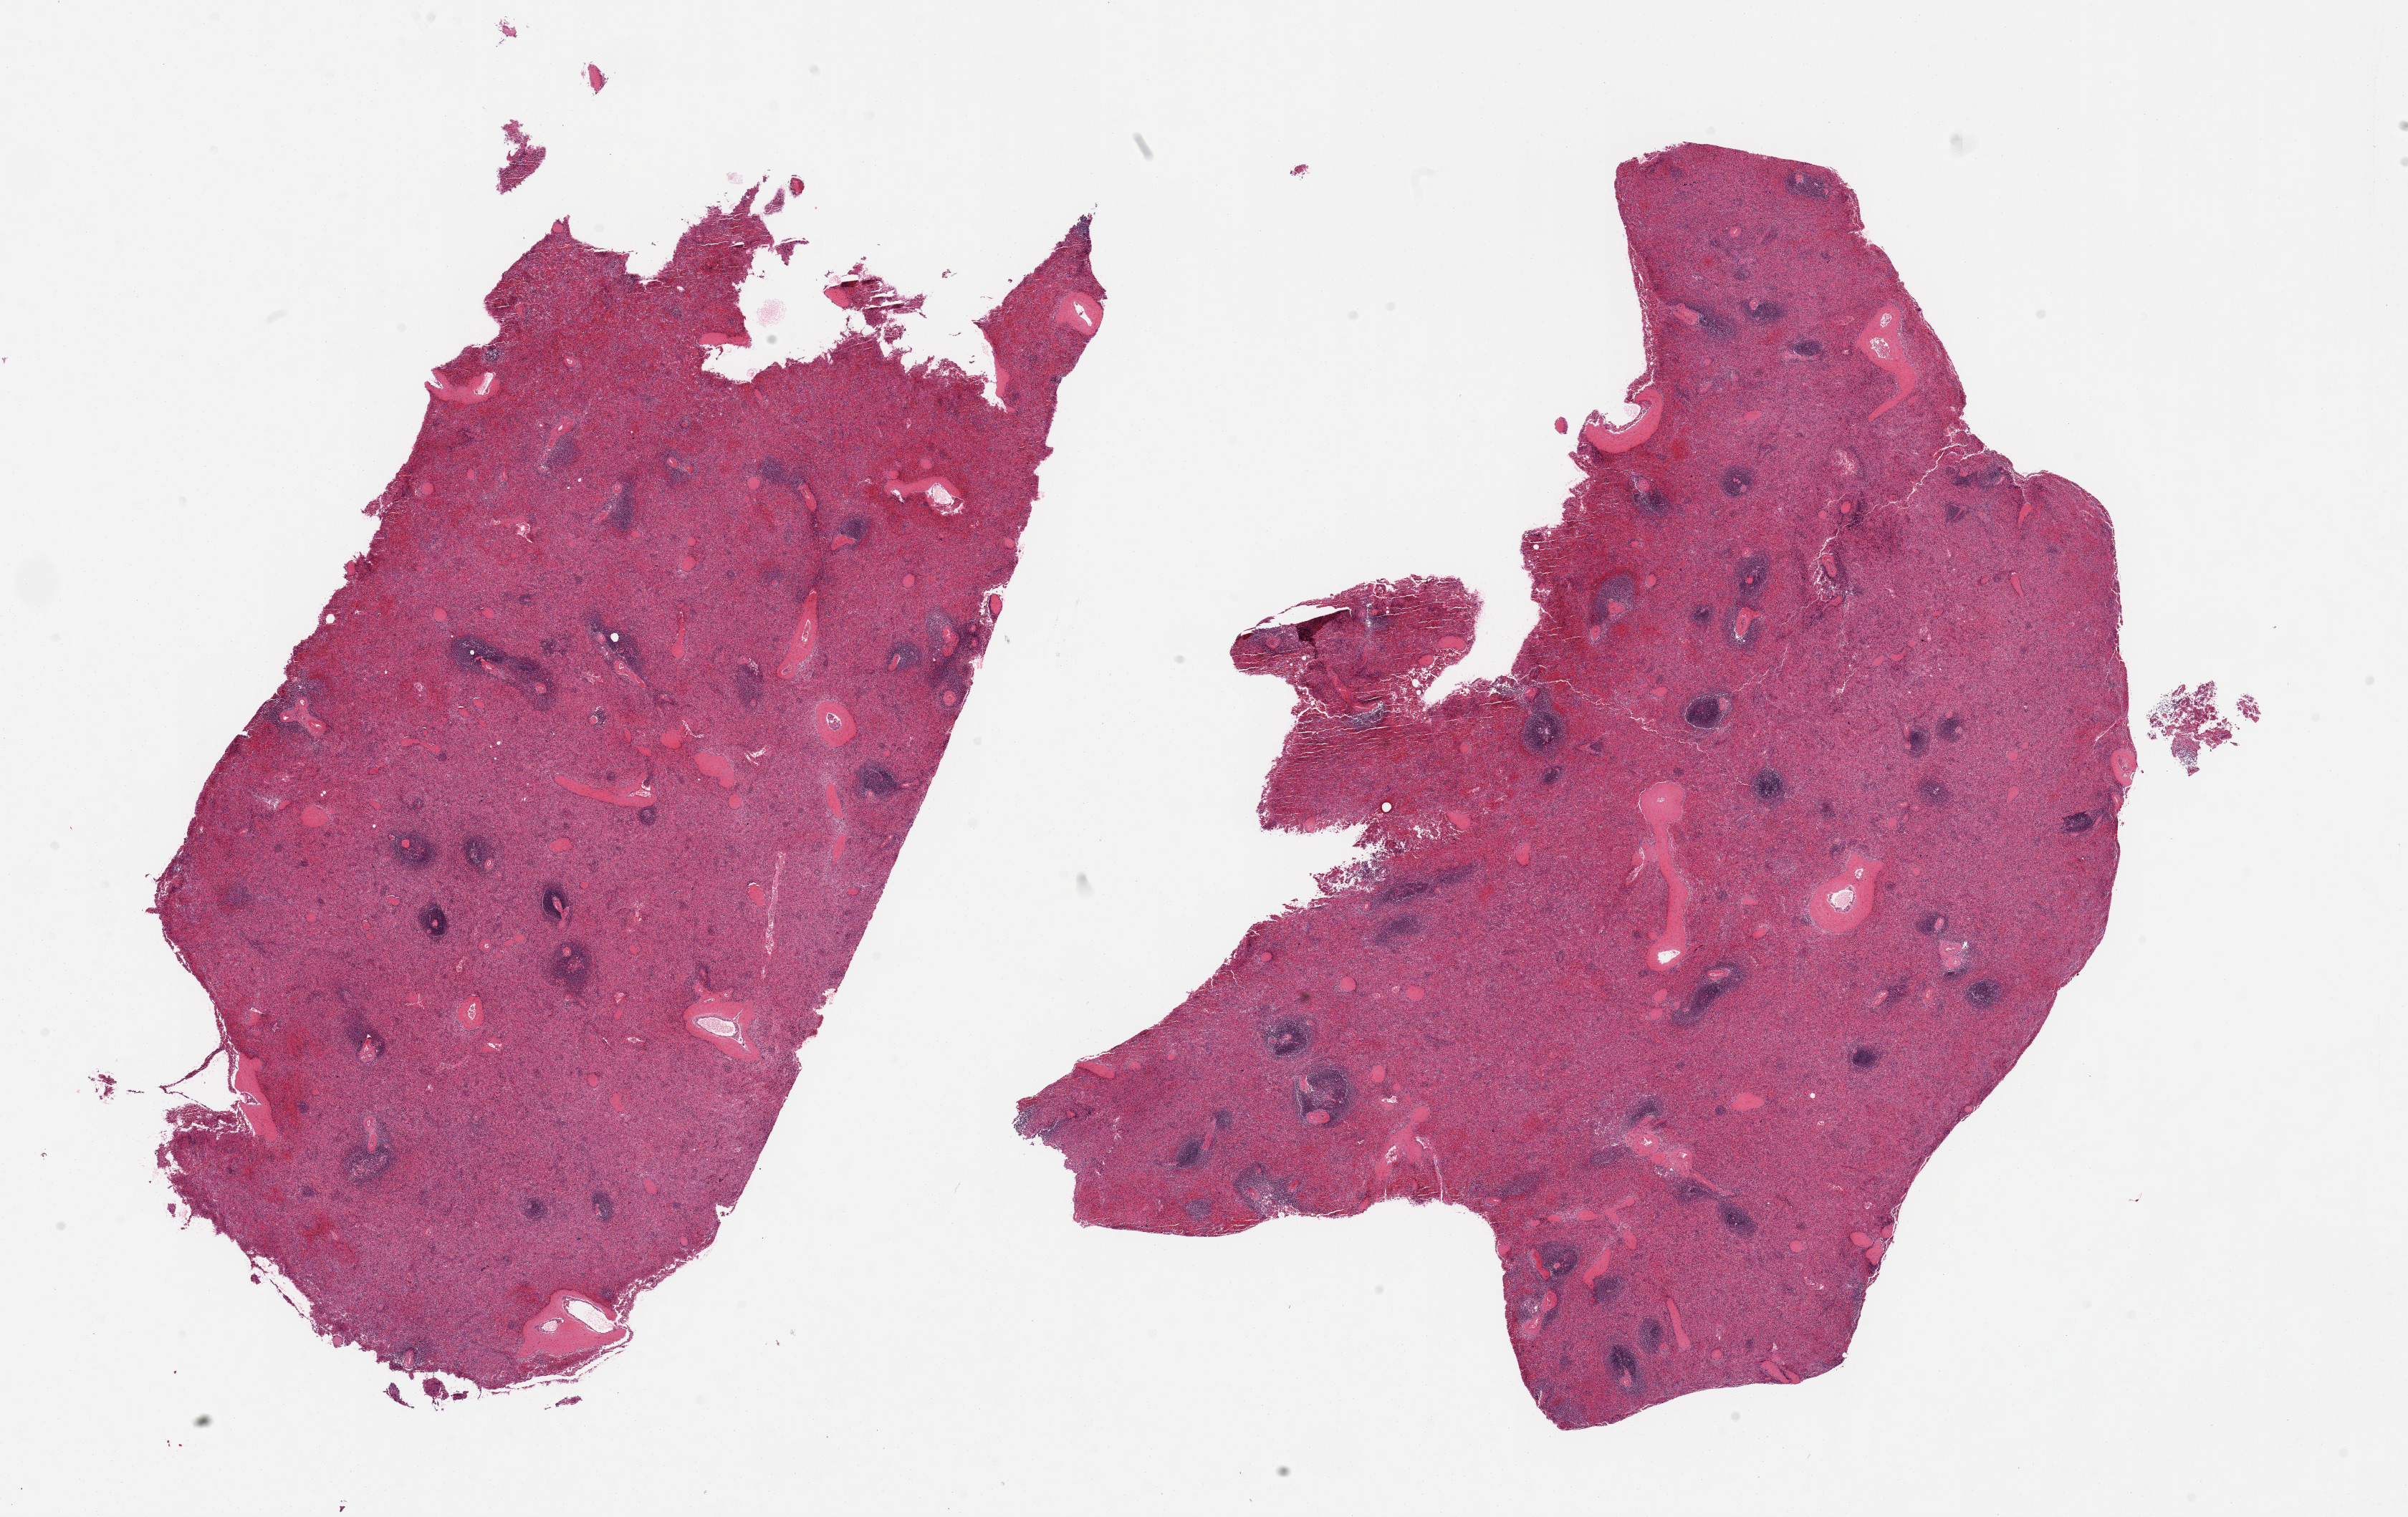
H&E whole-slide image, a low-resolution overview of the entire scanned area, about 26.6 x 16.7 mm. PAXgene-fixed, paraffin-embedded tissue. Sampled site (target tissue): spleen. Tissue donor sample. Donor sex: male.
Reviewer comment on this tissue sample: 2 pieces, moderate congestion.